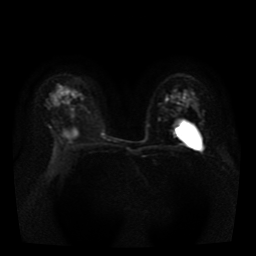
Breast MRI, one axial slice; slice 27 of 43 in the series (ordered by position); diffusion-weighted series; image 2 of 4 stored at this slice position (different b-values; order by instance number); 1.5 T; 256 × 256 image matrix, field of view 330 × 330 mm. Female patient.
Structures marked on this image (expert manual segmentation):
- tumour on diffusion-weighted imaging: bounding box <172,132,176,138> (left, top, right, bottom; pixels)